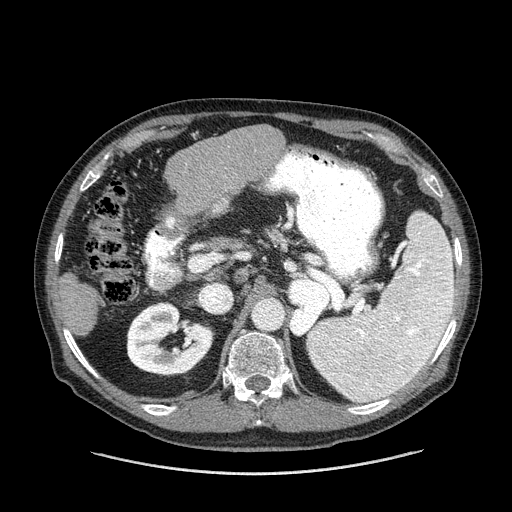
Contrast-enhanced abdominal CT (liver protocol), one axial slice. Slice 72 of 180 in the series (ordered by position). Reconstruction kernel STANDARD. 120 kVp. One of 2 acquisitions stored at this slice position. Soft-tissue window (W 400 / L 40 HU). 2.5 mm slice thickness. 512 × 512 image matrix, field of view 420 × 420 mm. From the clinical record (not read from this slice): diagnosis: hepatocellular carcinoma (patient treated with transarterial chemoembolisation; whether this scan precedes or follows treatment is not stated here); TNM stage (as recorded): Stage-II.
Outlined on this slice (semi-automatically segmented with operator editing):
- liver parenchyma outside the tumour (the mass and vessels are separate outlines, so this box may not span the whole liver): bounding box [x1, y1, x2, y2] px = [56, 126, 284, 336]